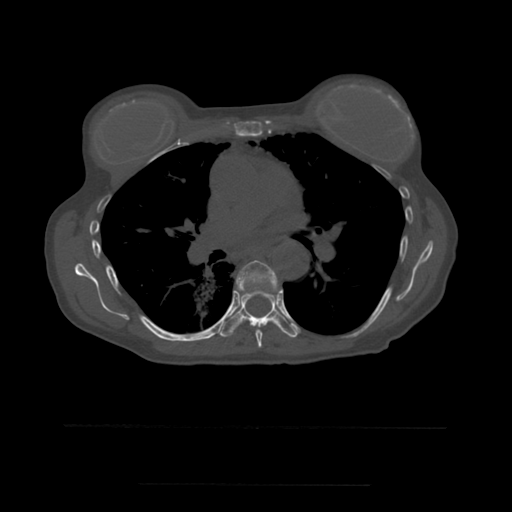
CT including the spine, one axial slice. Bone window (W 1800 / L 400 HU). 1.25 mm slice thickness. 512 × 512 image matrix, field of view 350 × 350 mm. Patient age 58 years. Case-level facts recorded for this patient, not image findings: primary cancer: lung.
Annotated regions visible in this slice (semi-automatic segmentation, software-assisted and operator-edited):
- T6 vertebra: bounding box (x1, y1, x2, y2) in pixels: (236, 260, 281, 348)
- T7 vertebra: (210, 288, 300, 338)